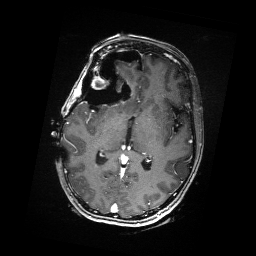
Brain MRI from a brain-tumour surgery series, one axial slice. T1-weighted post-contrast. 1 mm slice thickness. 256 × 256 image matrix. Case-level facts recorded for this patient, not image findings: histopathology: Metastatic Carcinoma from Breast primary; tumour location: Right Frontal.
Outlined on this slice (outlined manually by an expert reader):
- residual tumour: box from (x=88, y=69) to (x=117, y=88) px